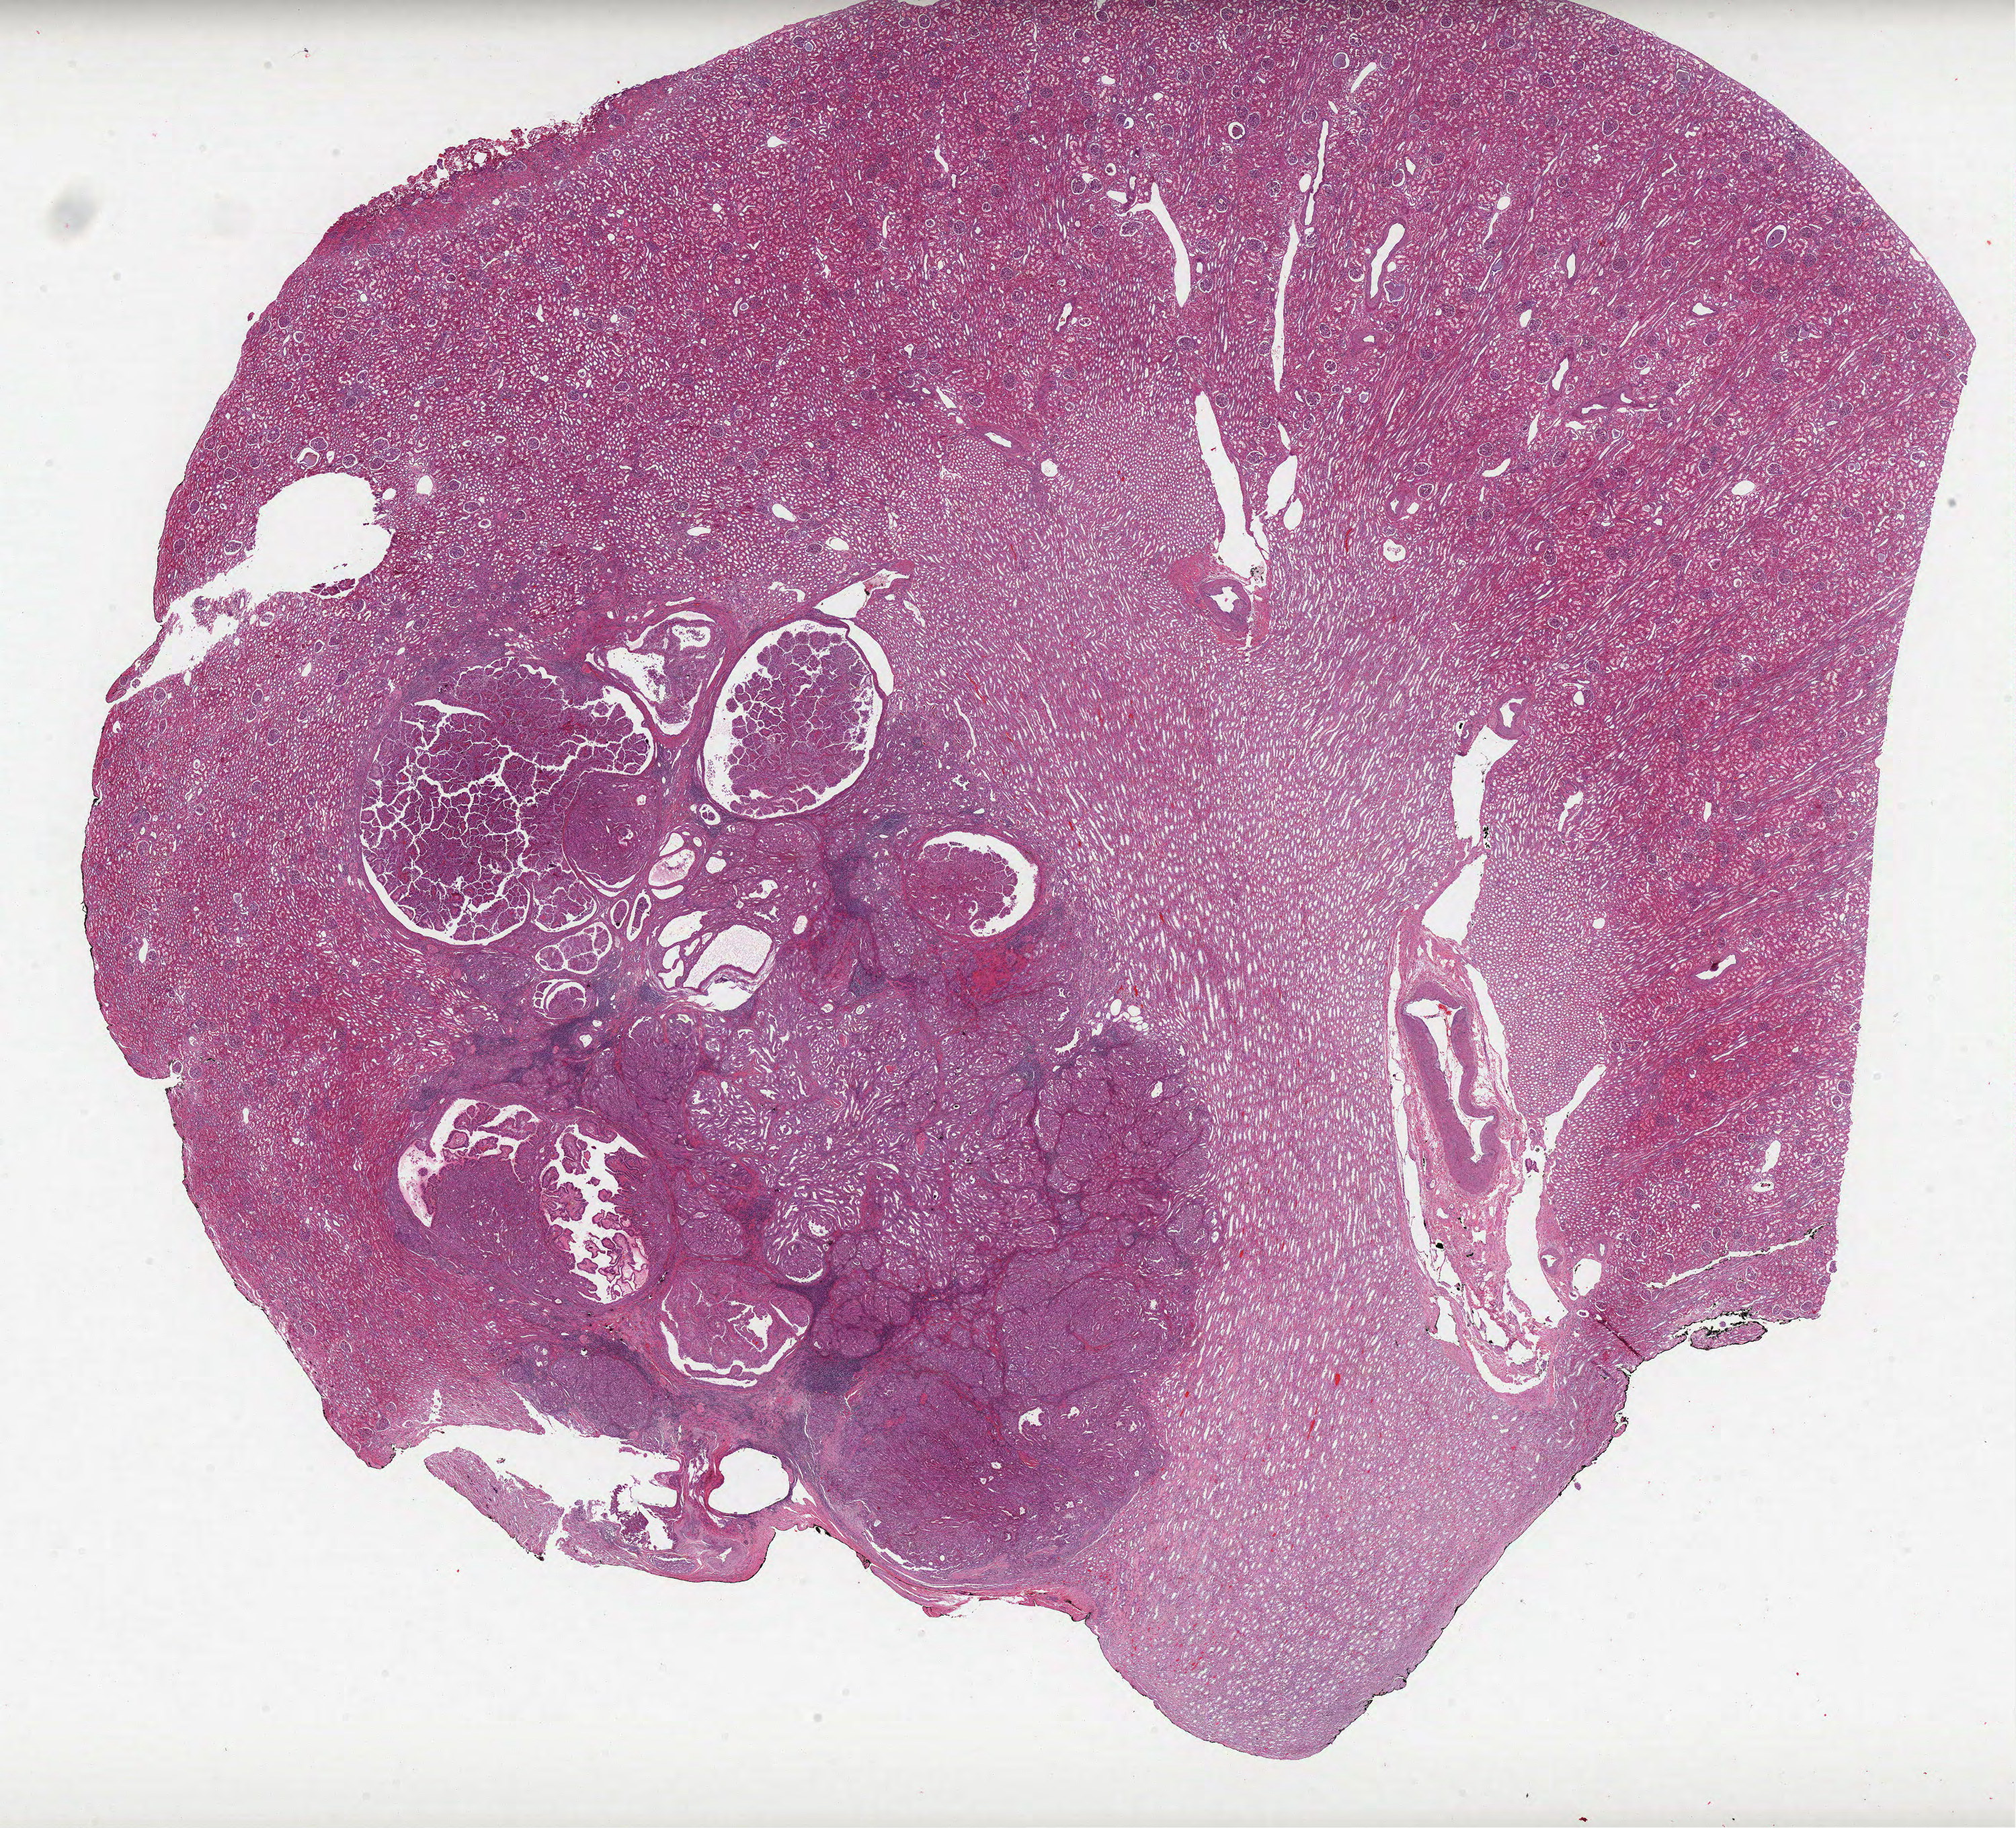
Hematoxylin and eosin (H&E) stained whole-slide image — shown as a low-resolution overview of the whole scanned area (about 24.0 x 21.7 mm, acquisition: 40x scan), formalin-fixed paraffin-embedded (FFPE) diagnostic section, kidney, primary tumour sample. Female patient; age at initial diagnosis 57 years.
- diagnosis: Papillary adenocarcinoma, NOS
- AJCC pathologic stage: III (6th edition)